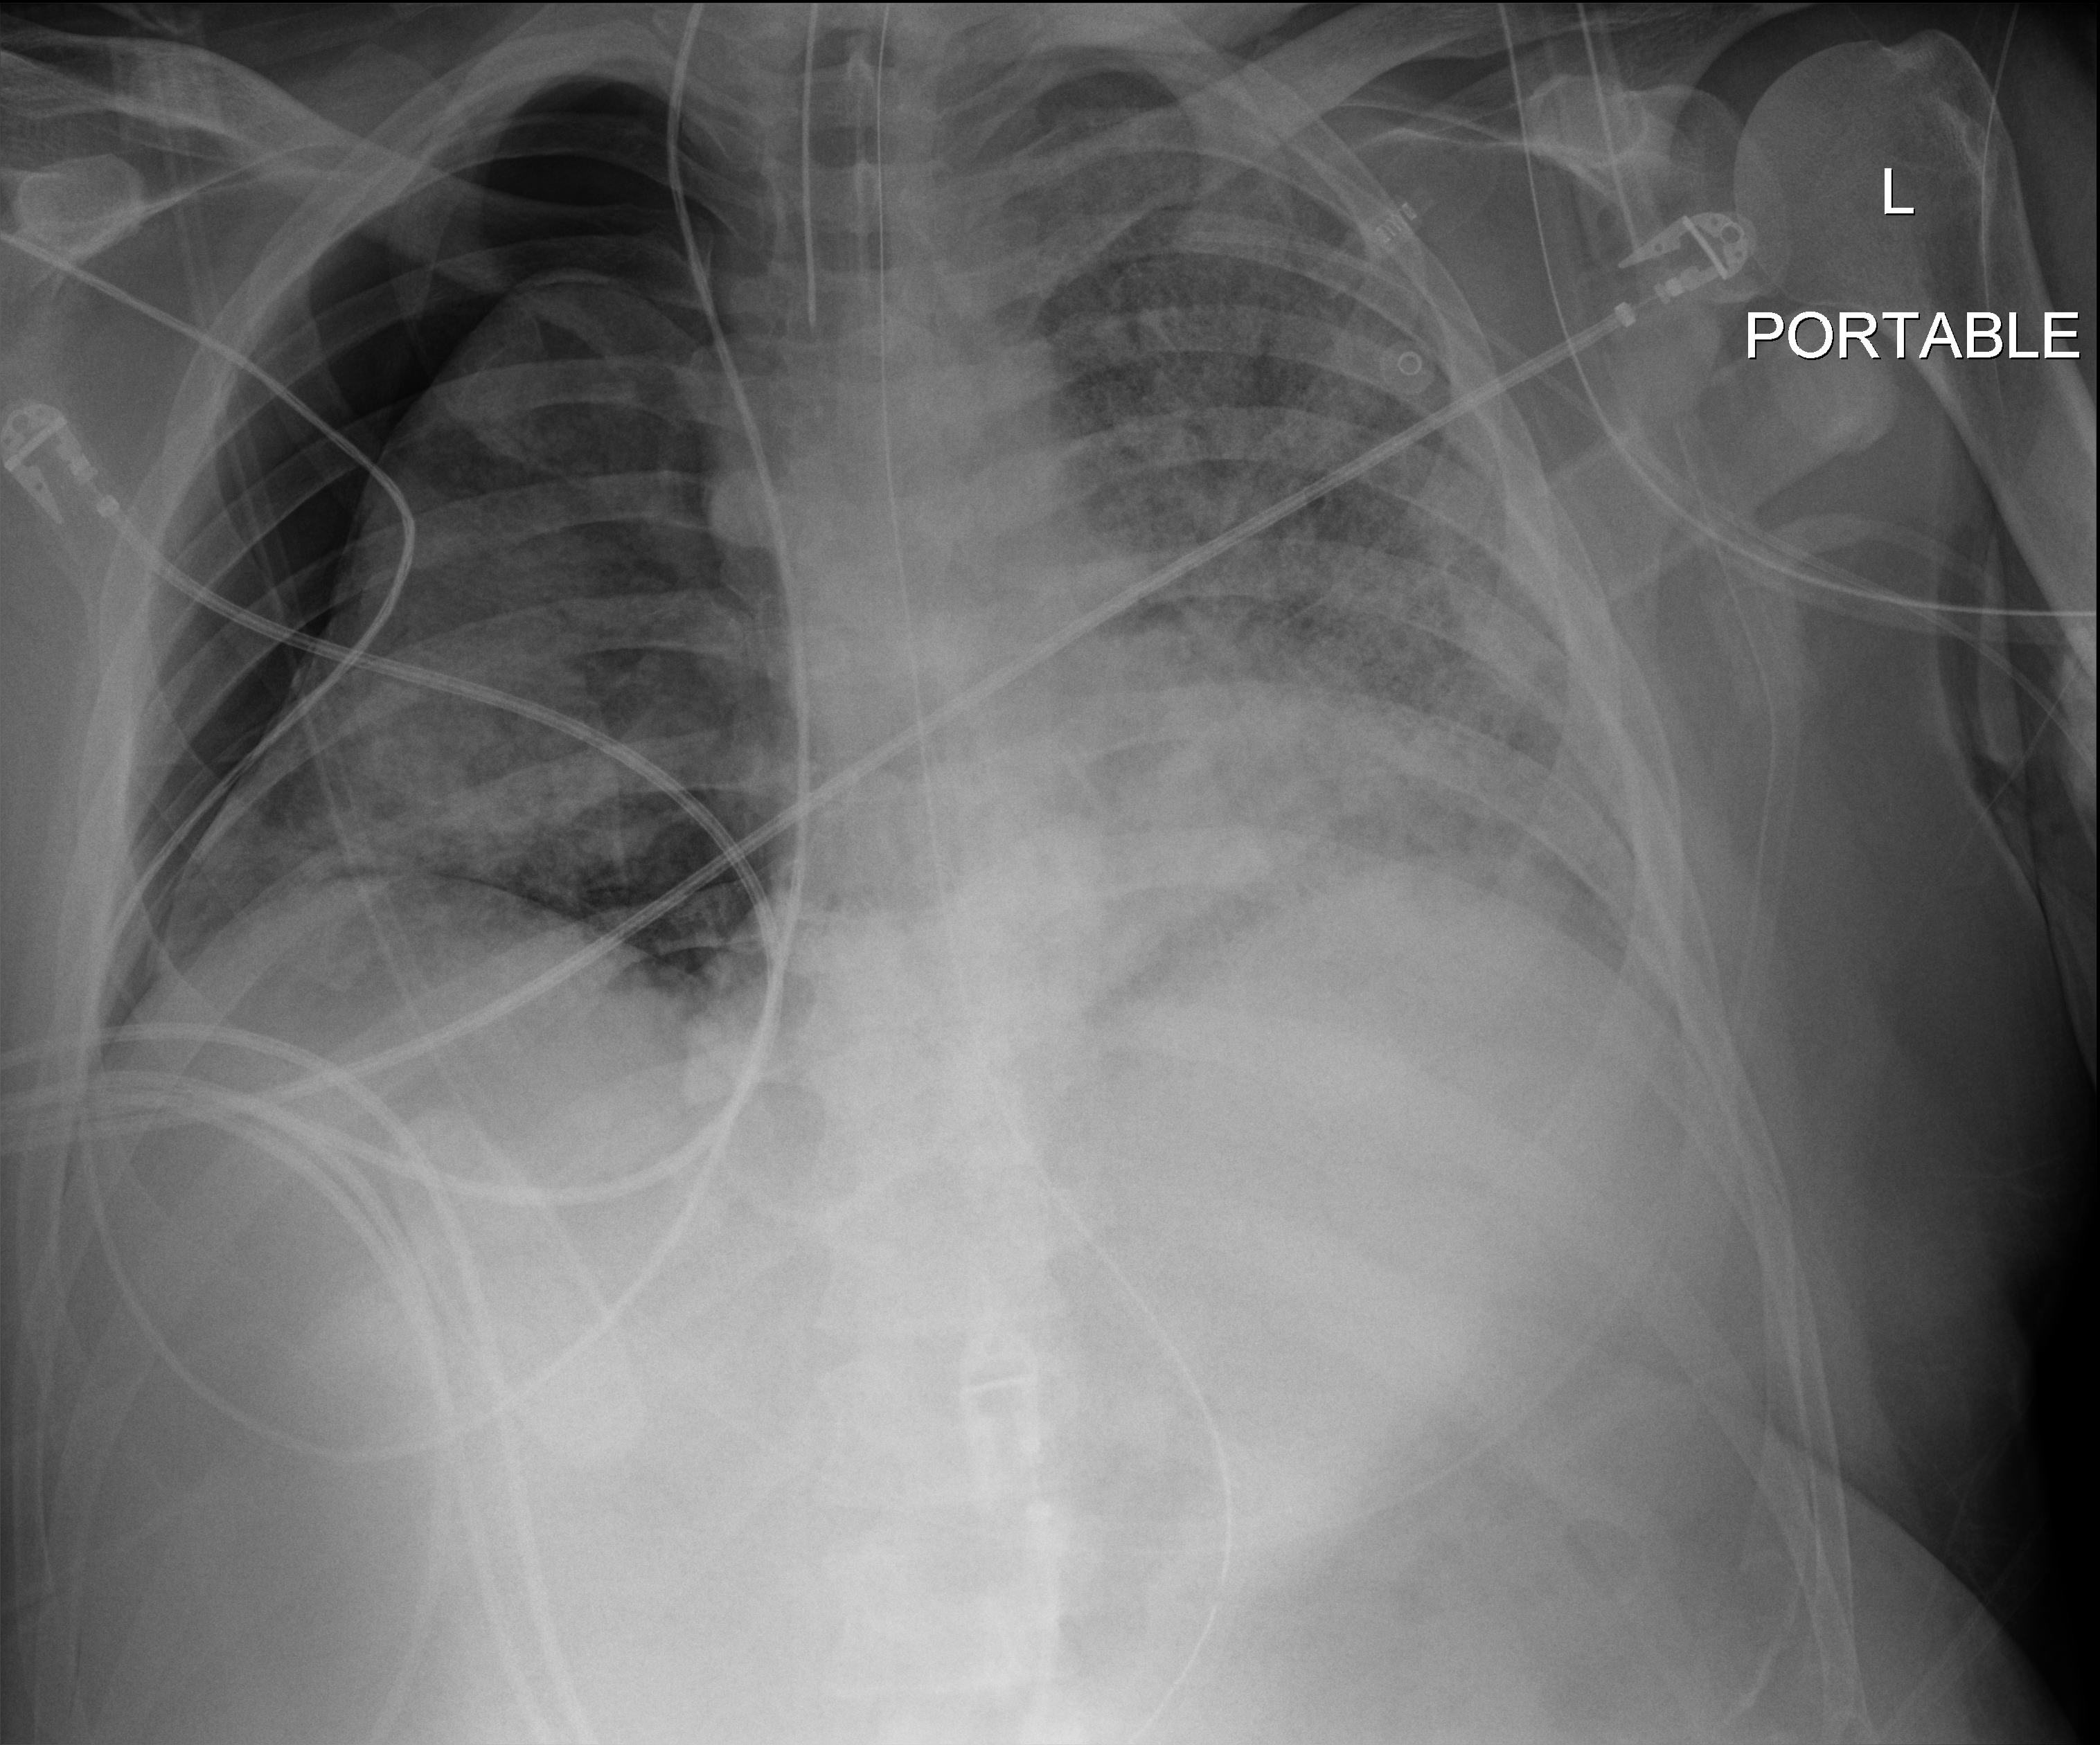
Bedside chest radiograph (digital radiography); anteroposterior (AP) projection. Male patient hospitalised with COVID-19, age 18–59 years.
From the hospital-stay record, not from the radiograph (when in the stay this image was taken is not recorded):
- other chronic lung disease (admission record): no
- mechanically ventilated during this hospital stay: yes
- diabetes (admission record): no